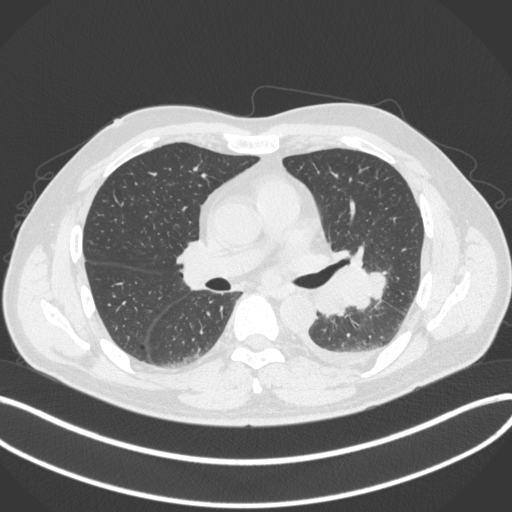
Chest CT, one axial slice. Slice 201 of 350 in the series (ordered by position). Reconstruction kernel B31f. 120 kVp. Lung window (W 1500 / L -600 HU). 512 × 512 image matrix. Patient: male, 58 years. Case-level facts recorded for this patient, not image findings: clinical TNM (as recorded): T3 N1 M1b.
Structures marked on this image (rectangle marked by the reading radiologist):
- lung tumour (recorded histology: small cell carcinoma): bounding box <314,249,394,319> (left, top, right, bottom; pixels)